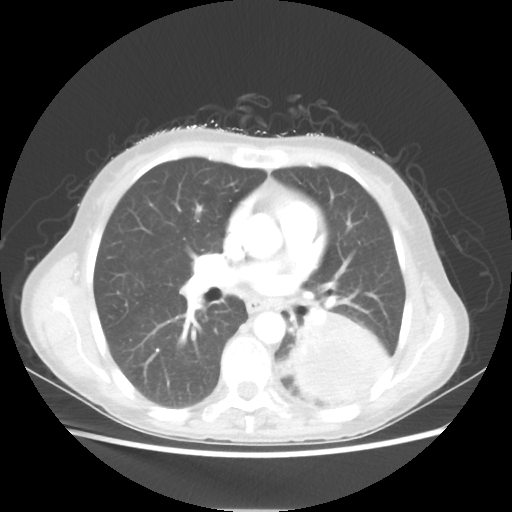
Chest CT, one axial slice; slice 30 of 56 in the series (ordered by position); lung window (W 1500 / L -600 HU); 5 mm slice thickness; 512 × 512 image matrix, field of view 360 × 360 mm. Patient: female, 53 years. Case-level facts recorded for this patient, not image findings: clinical TNM (as recorded): T3 N0 M0.
Annotated regions visible in this slice (rectangle marked by the reading radiologist):
- lung tumour (recorded histology: adenocarcinoma): box from (x=284, y=311) to (x=392, y=403) px